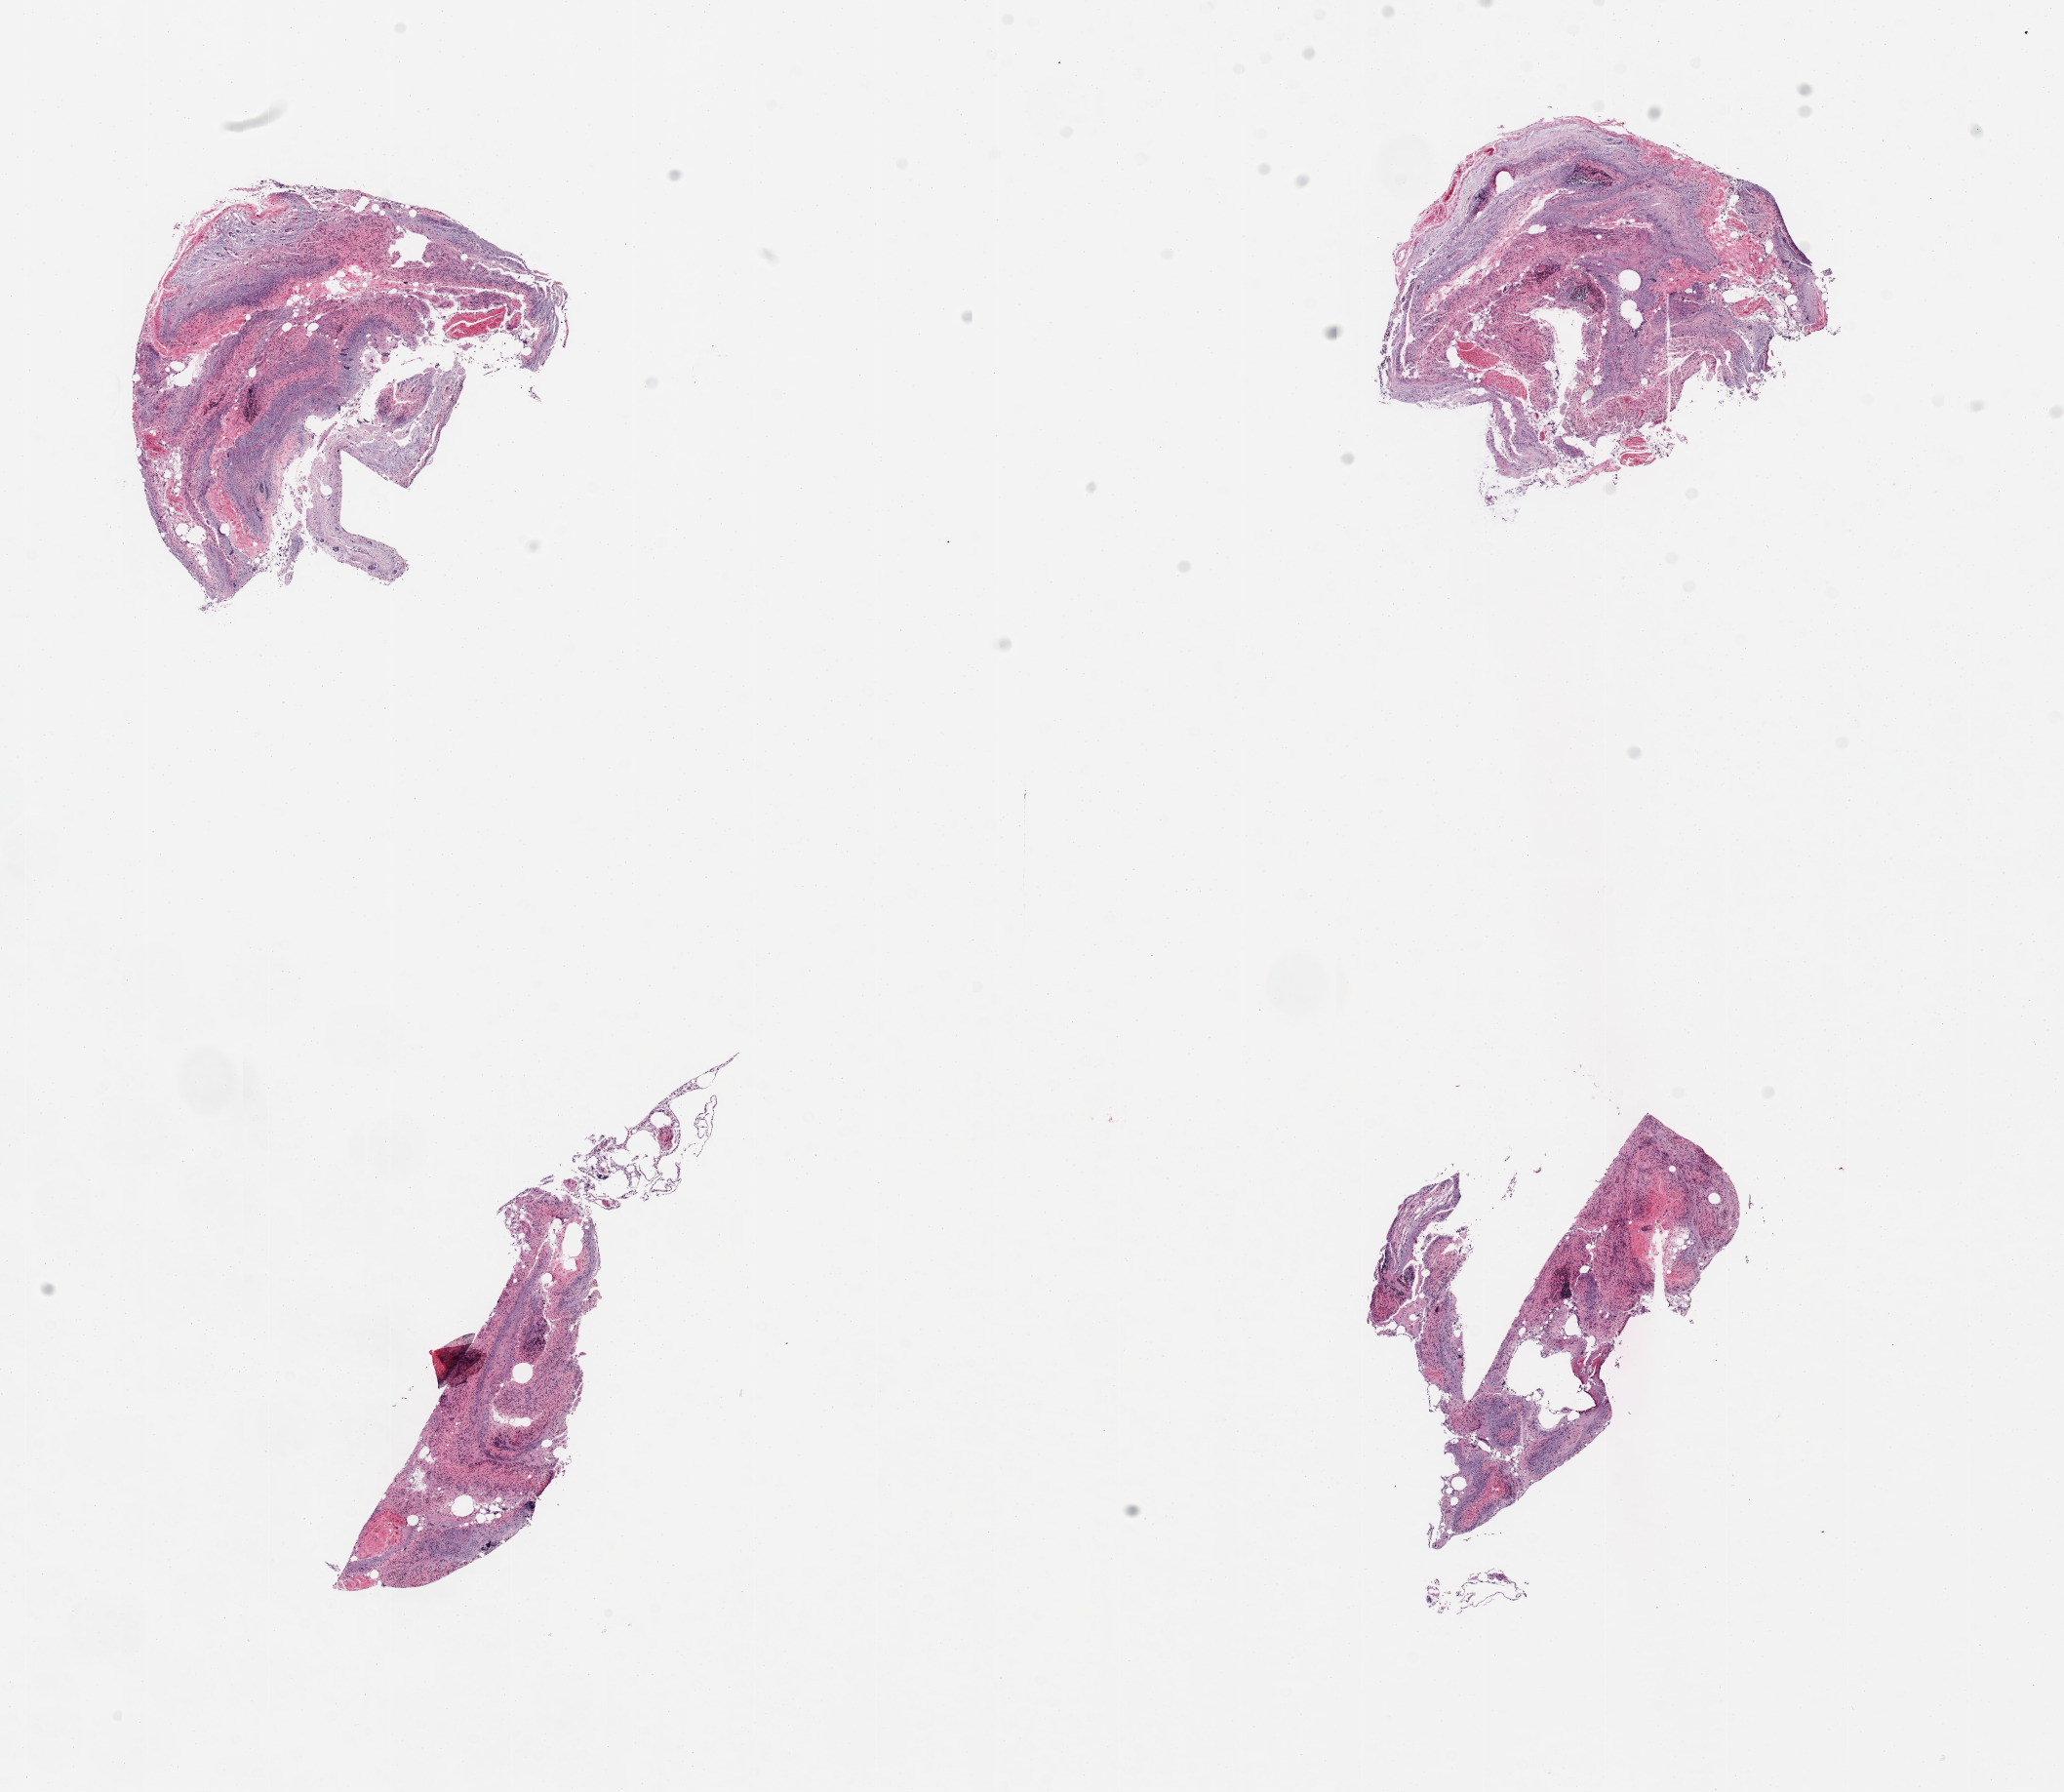
Haematoxylin and eosin whole-slide image, a low-resolution overview of the entire scanned area, about 16.7 x 14.5 mm; PAXgene-fixed, paraffin-embedded tissue; sampled site (target tissue): ileum; tissue donor sample. Female donor.
• review note (as recorded): 4 pieces; totally autolyzed; no visible lymphoid nodules